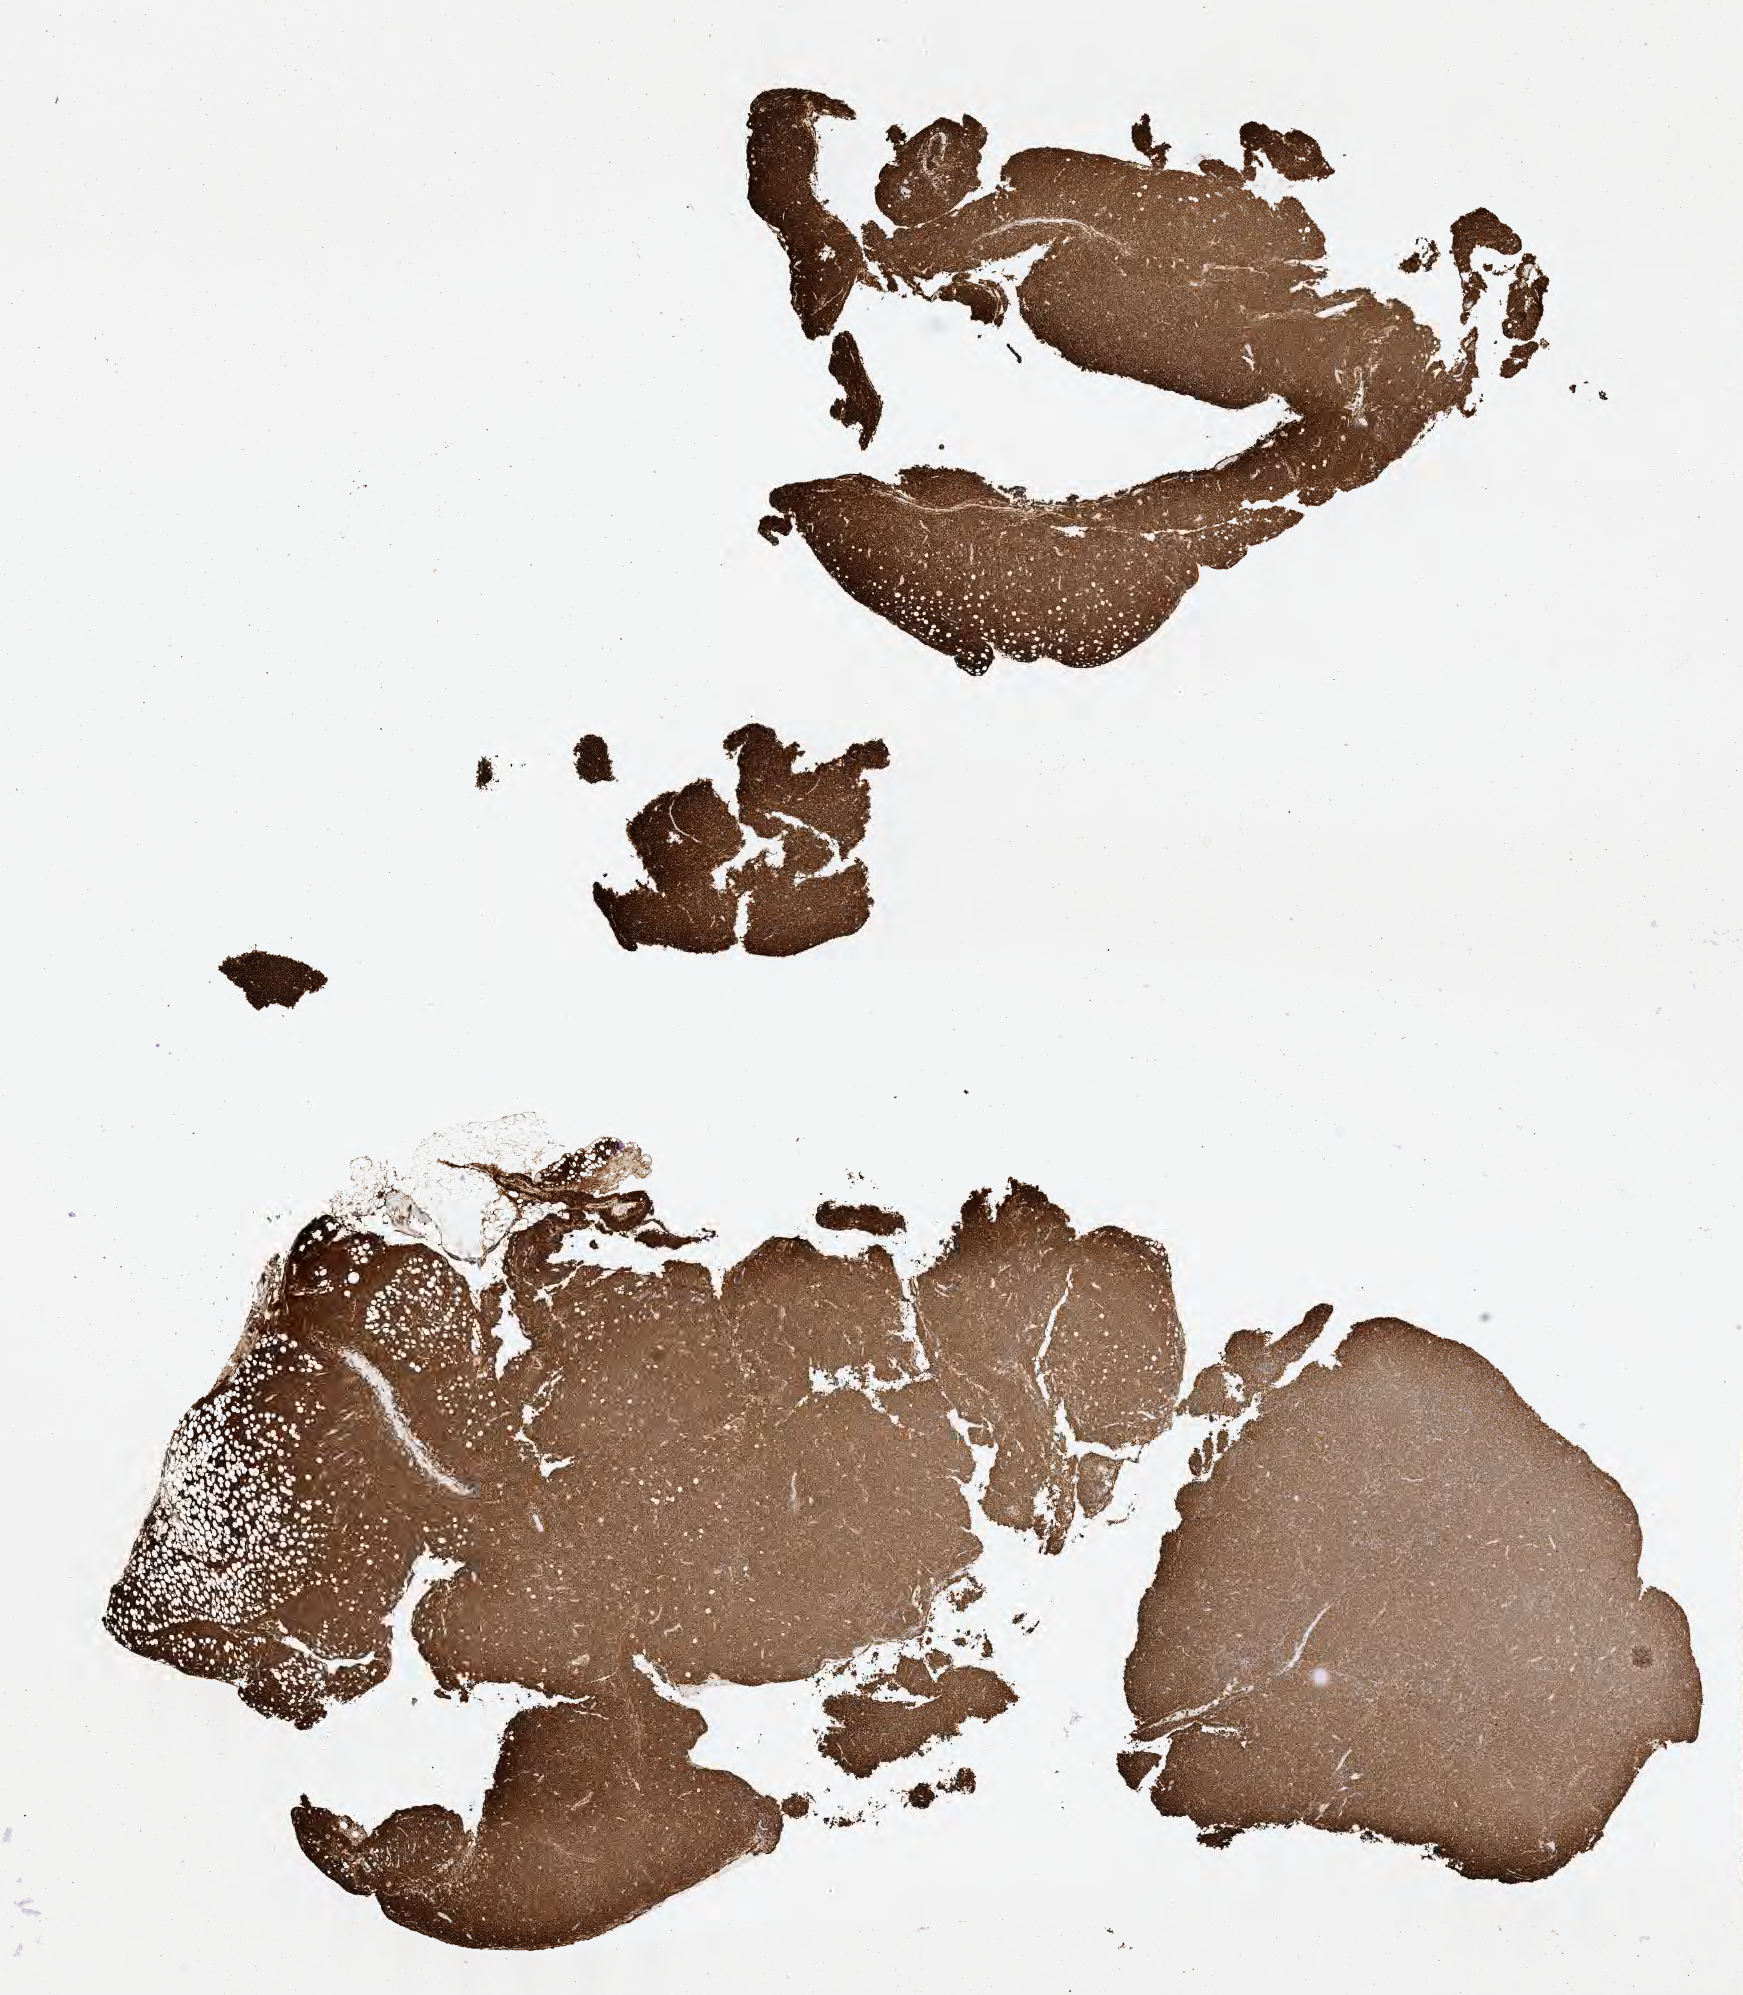
IHC for CD20, whole-slide image — whole scanned area (about 14.1 x 16.1 mm) shown as a low-resolution overview. Specimen: tumor tissue. Female patient, age 32 years.
Histologic diagnosis: Diffuse large B-cell lymphoma, NOS.